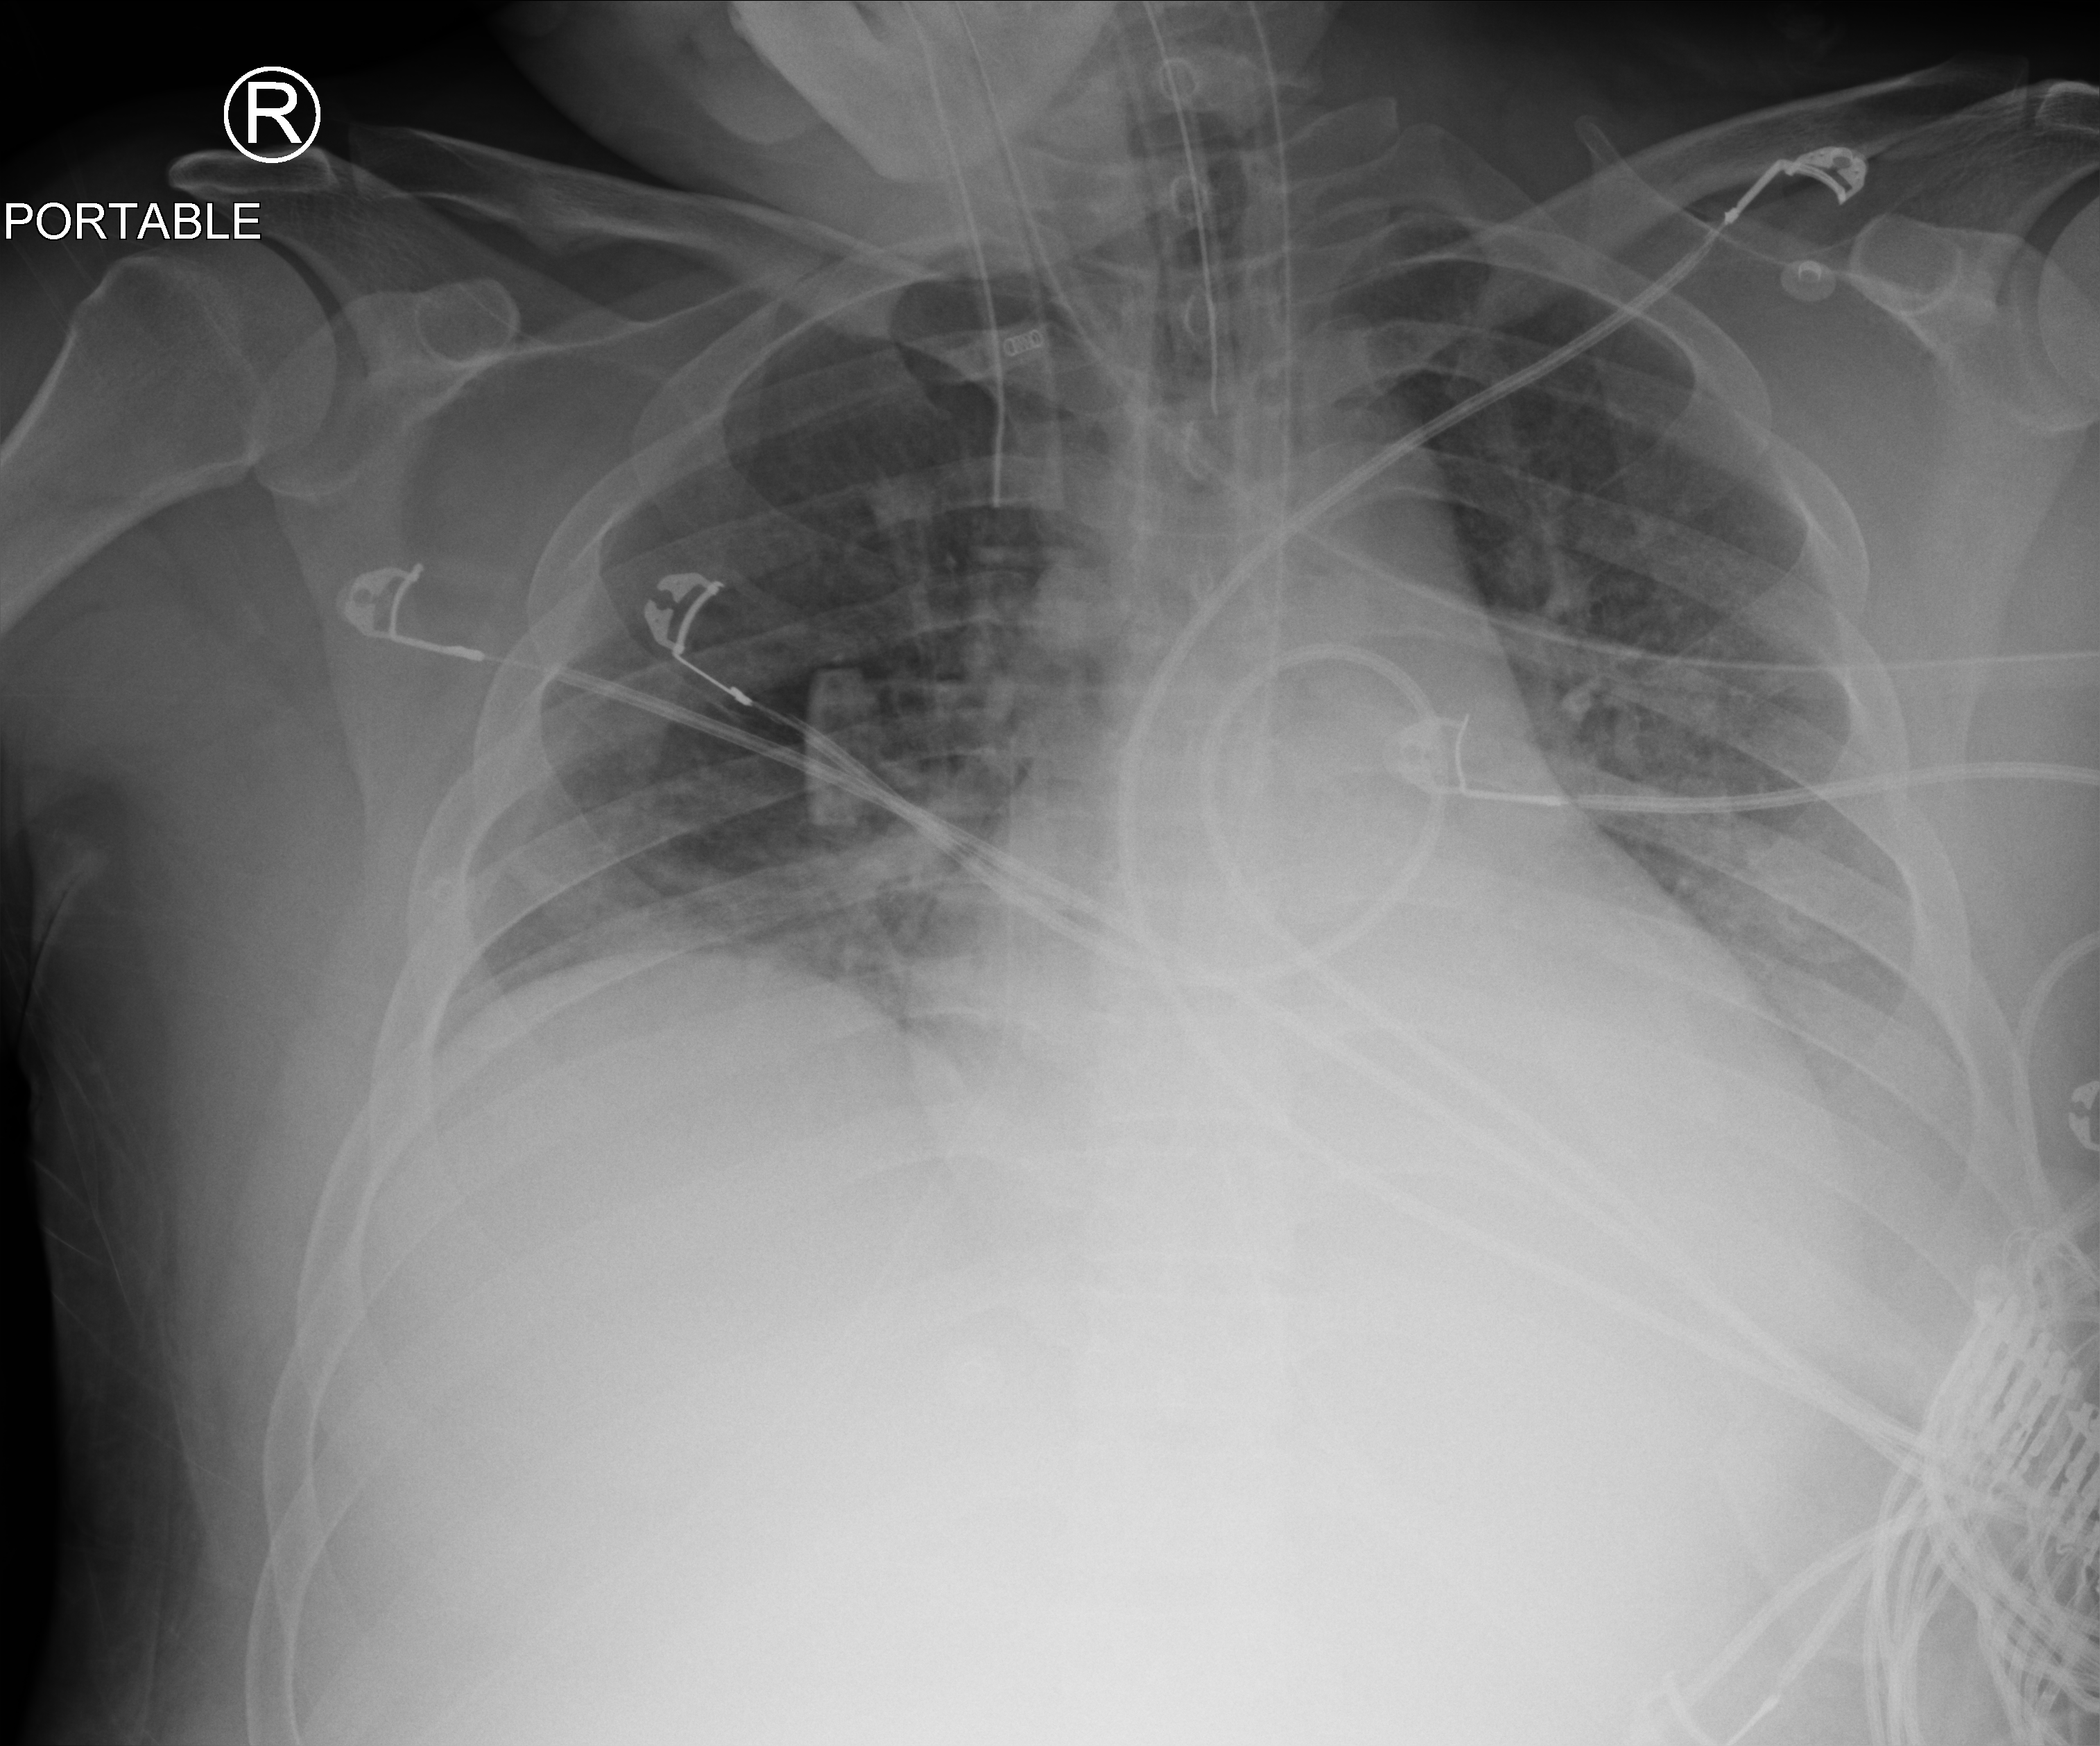
Portable chest radiograph, anteroposterior (AP) projection. Male patient hospitalised with COVID-19, age 18–59 years.
Admission-level facts for this patient (not findings on this image; timing relative to this image not recorded):
- mechanically ventilated during this hospital stay: yes
- hypertension (admission record): yes
- length of hospital stay: 61 days